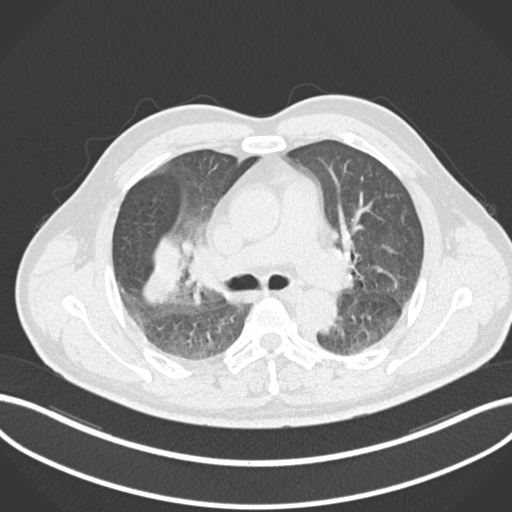
Chest CT, one axial slice; position 642 of 852 along the scan axis; reconstruction kernel B30f; lung window (W 1500 / L -600 HU); 1 mm slice thickness; 512 × 512 image matrix, field of view 400 × 400 mm. Patient: male, 55 years. Case-level facts recorded for this patient, not image findings: clinical TNM (as recorded): T3 N2 M1.
Annotated regions visible in this slice (rectangle marked by the reading radiologist):
- lung tumour (recorded histology: adenocarcinoma): bounding box [x1, y1, x2, y2] px = [138, 236, 182, 309]